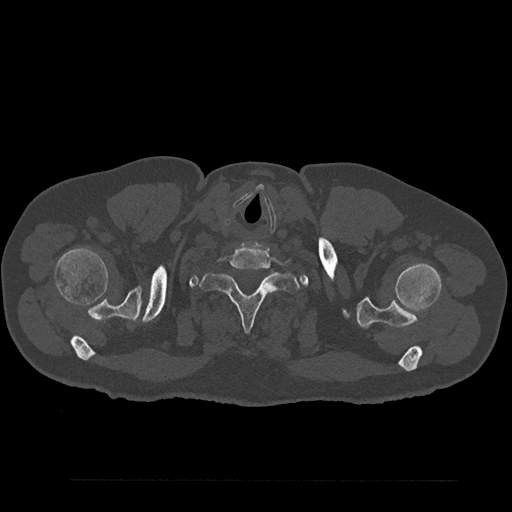
CT including the spine, one axial slice. Slice 759 of 797 in the series (ordered by position). 120 kVp. Bone window (W 1800 / L 400 HU). 0.5 mm slice thickness. 512 × 512 image matrix, field of view 430 × 430 mm. Patient: male, 61 years. Case-level facts recorded for this patient, not image findings: primary cancer: prostate.
Outlined on this slice (semi-automatic segmentation, software-assisted and operator-edited):
- T1 vertebra: bounding box (x1, y1, x2, y2) in pixels: (199, 261, 300, 332)